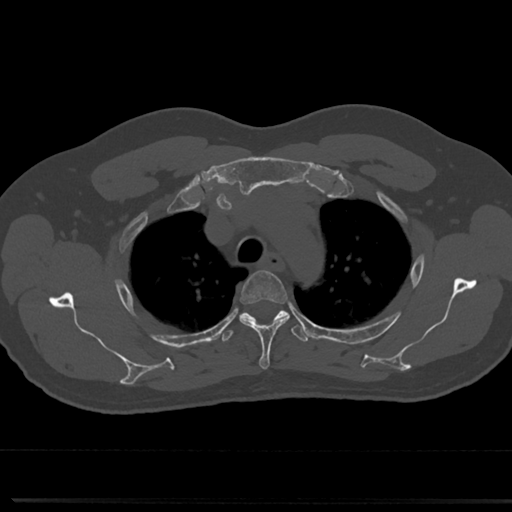
CT including the spine, one axial slice; position 575 of 817 along the scan axis; reconstruction kernel Br40s/3; bone window (W 1800 / L 400 HU); 512 × 512 image matrix. Patient: male, 61 years. Case-level facts recorded for this patient, not image findings: primary cancer: prostate.
Structures marked on this image (semi-automatically segmented with operator editing):
- T3 vertebra: bounding box <239,271,288,370> (left, top, right, bottom; pixels)
- T4 vertebra: <220,306,310,345>